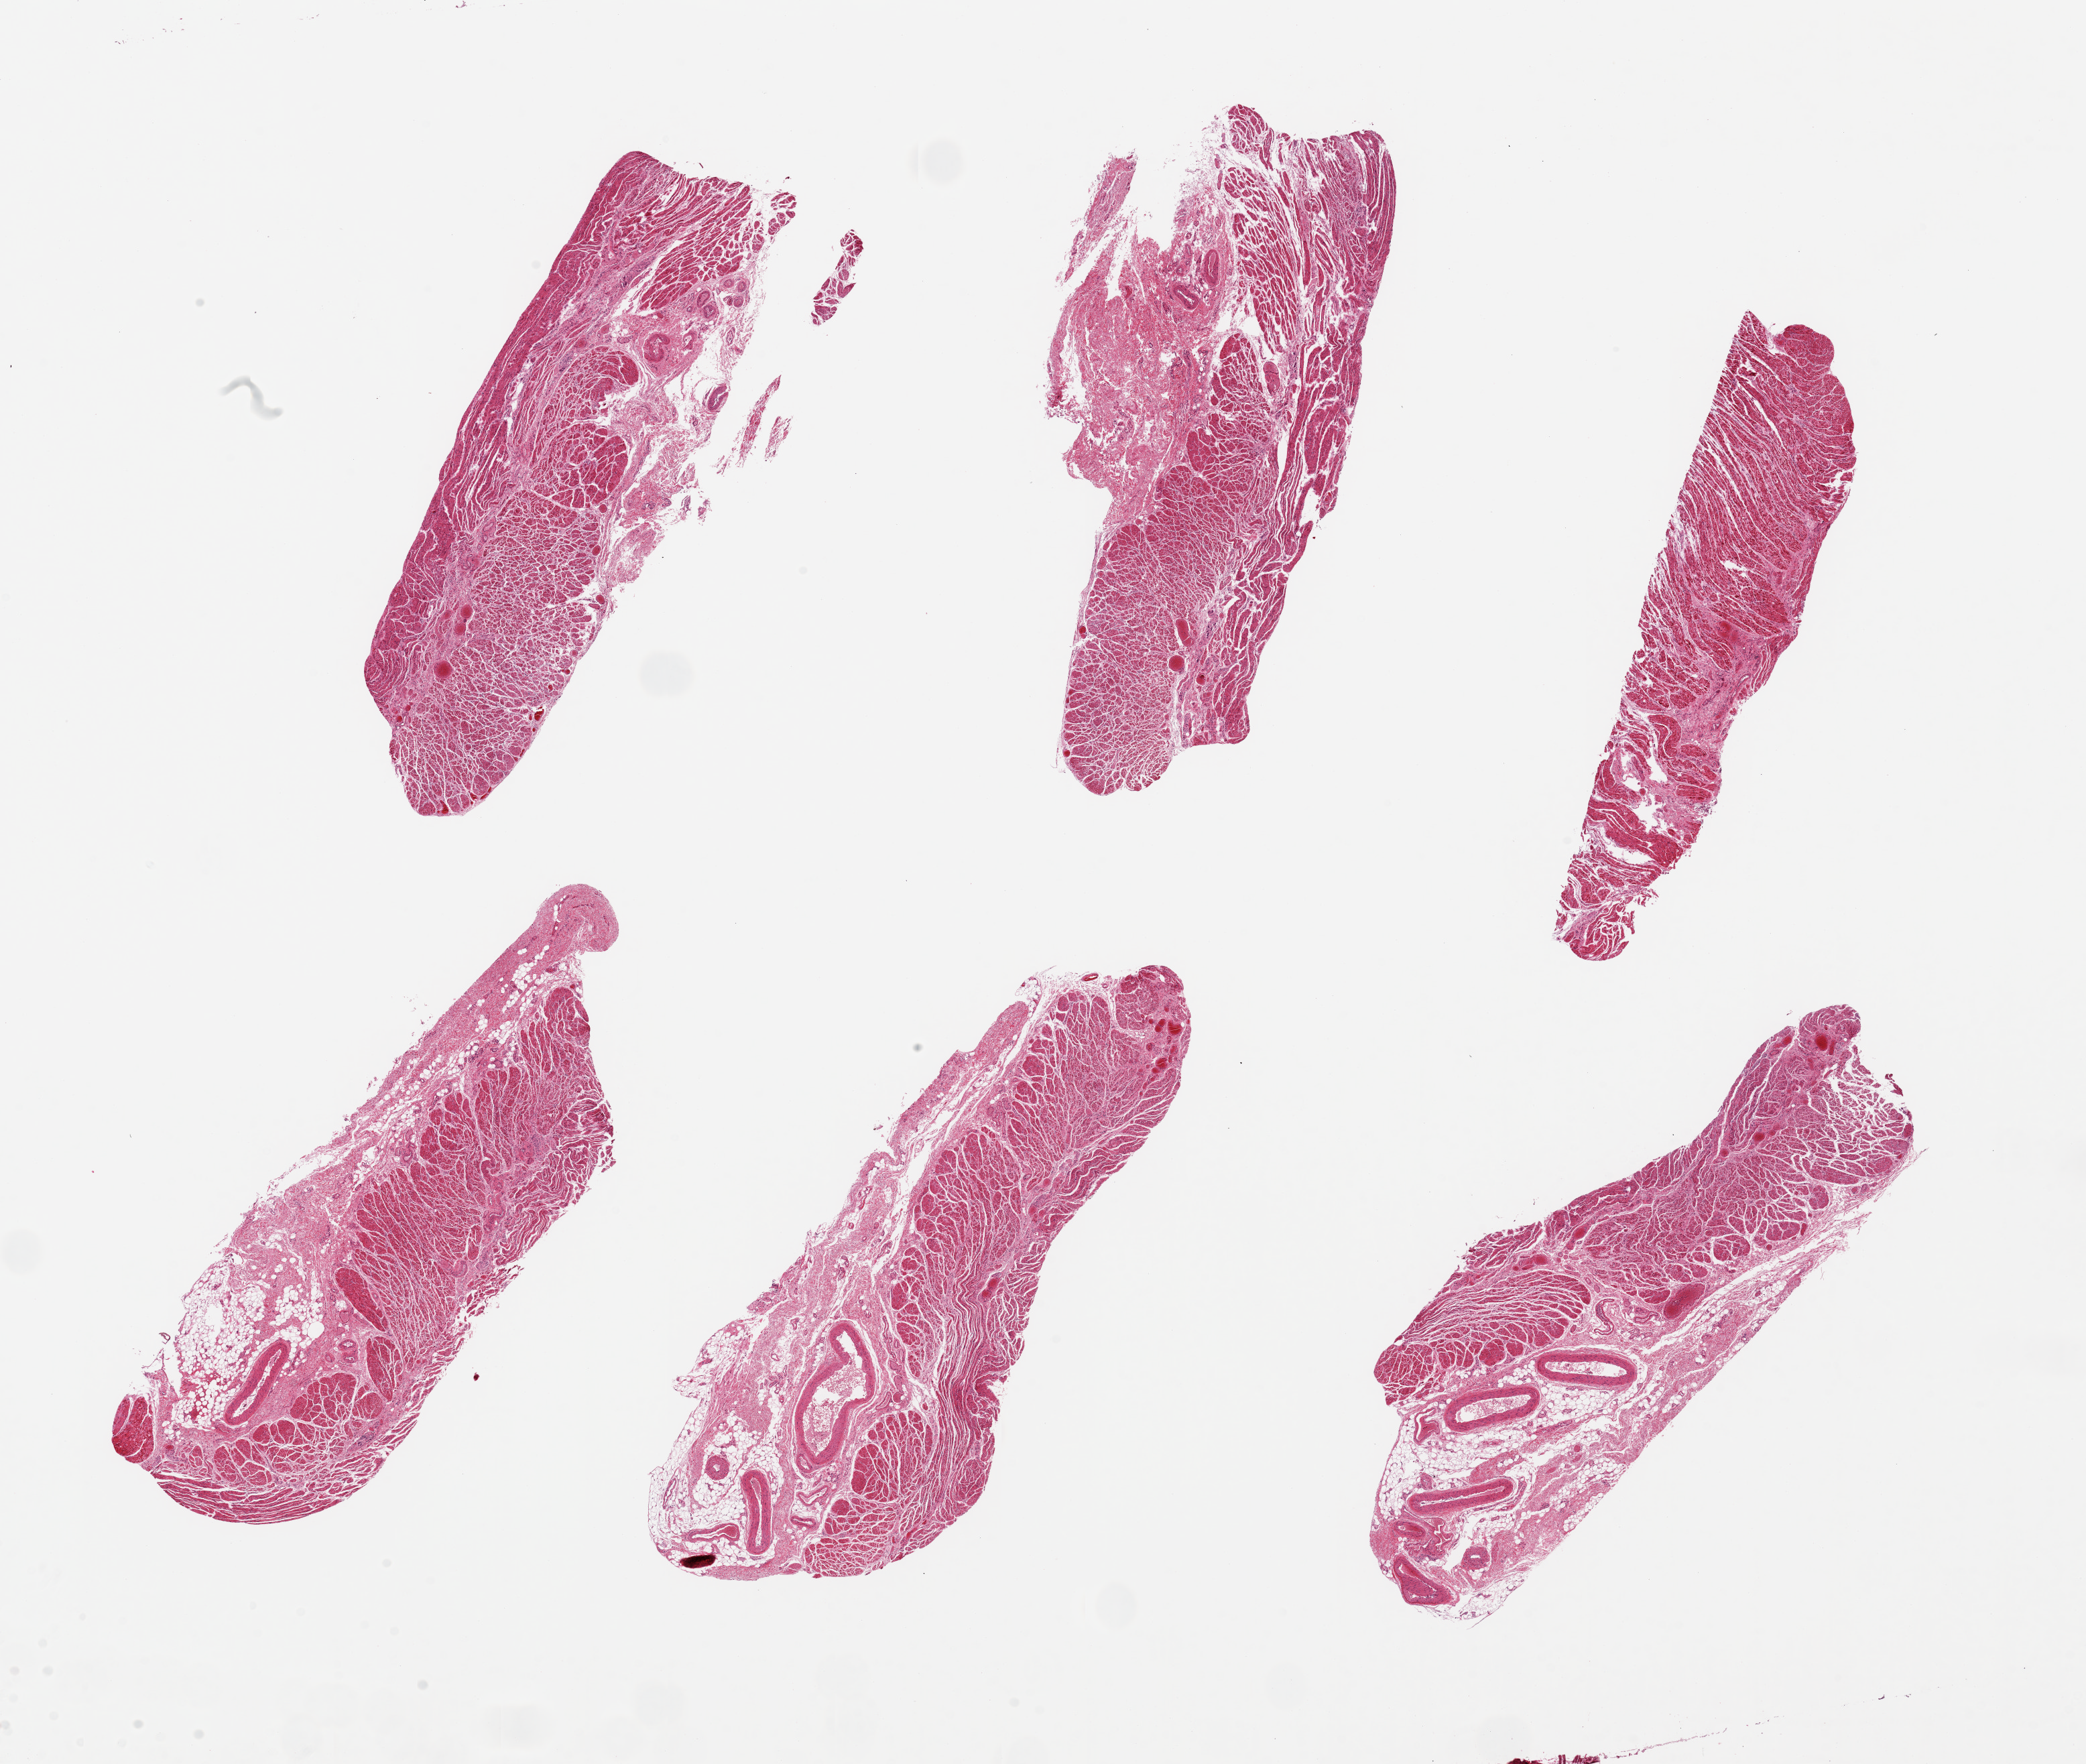
Haematoxylin and eosin whole-slide image — shown as a low-resolution overview of the whole scanned area (about 24.6 x 20.8 mm); PAXgene-fixed paraffin-embedded (PFPE) section; section of gastroesophageal junction (target tissue); donor tissue sample. Male donor.
* reviewer comment on this tissue sample: 6 pieces, up to 9x4mm; 1 has ~40% adipose, other 5 have well dissected muscularis